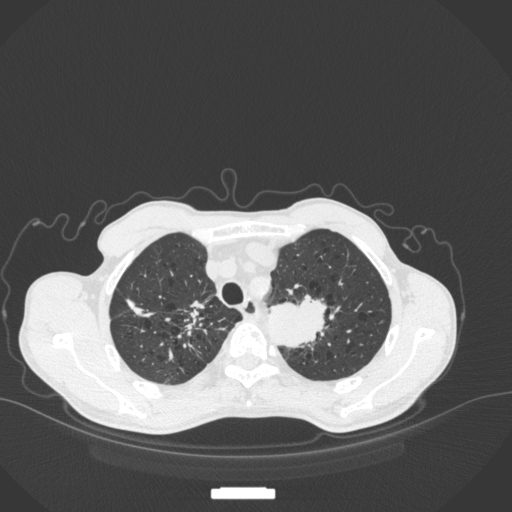
Chest CT, one axial slice; slice 348 of 394 in the series (ordered by position); lung window (W 1500 / L -600 HU); 1 mm slice thickness; 512 × 512 image matrix, field of view 400 × 400 mm. Male patient, age 65 years. From the clinical record (not read from this slice): clinical TNM (as recorded): T2b N0 M0.
Outlined on this slice (bounding box drawn by a radiologist):
- lung tumour (recorded histology: adenocarcinoma): bounding box [x1, y1, x2, y2] px = [267, 291, 330, 353]